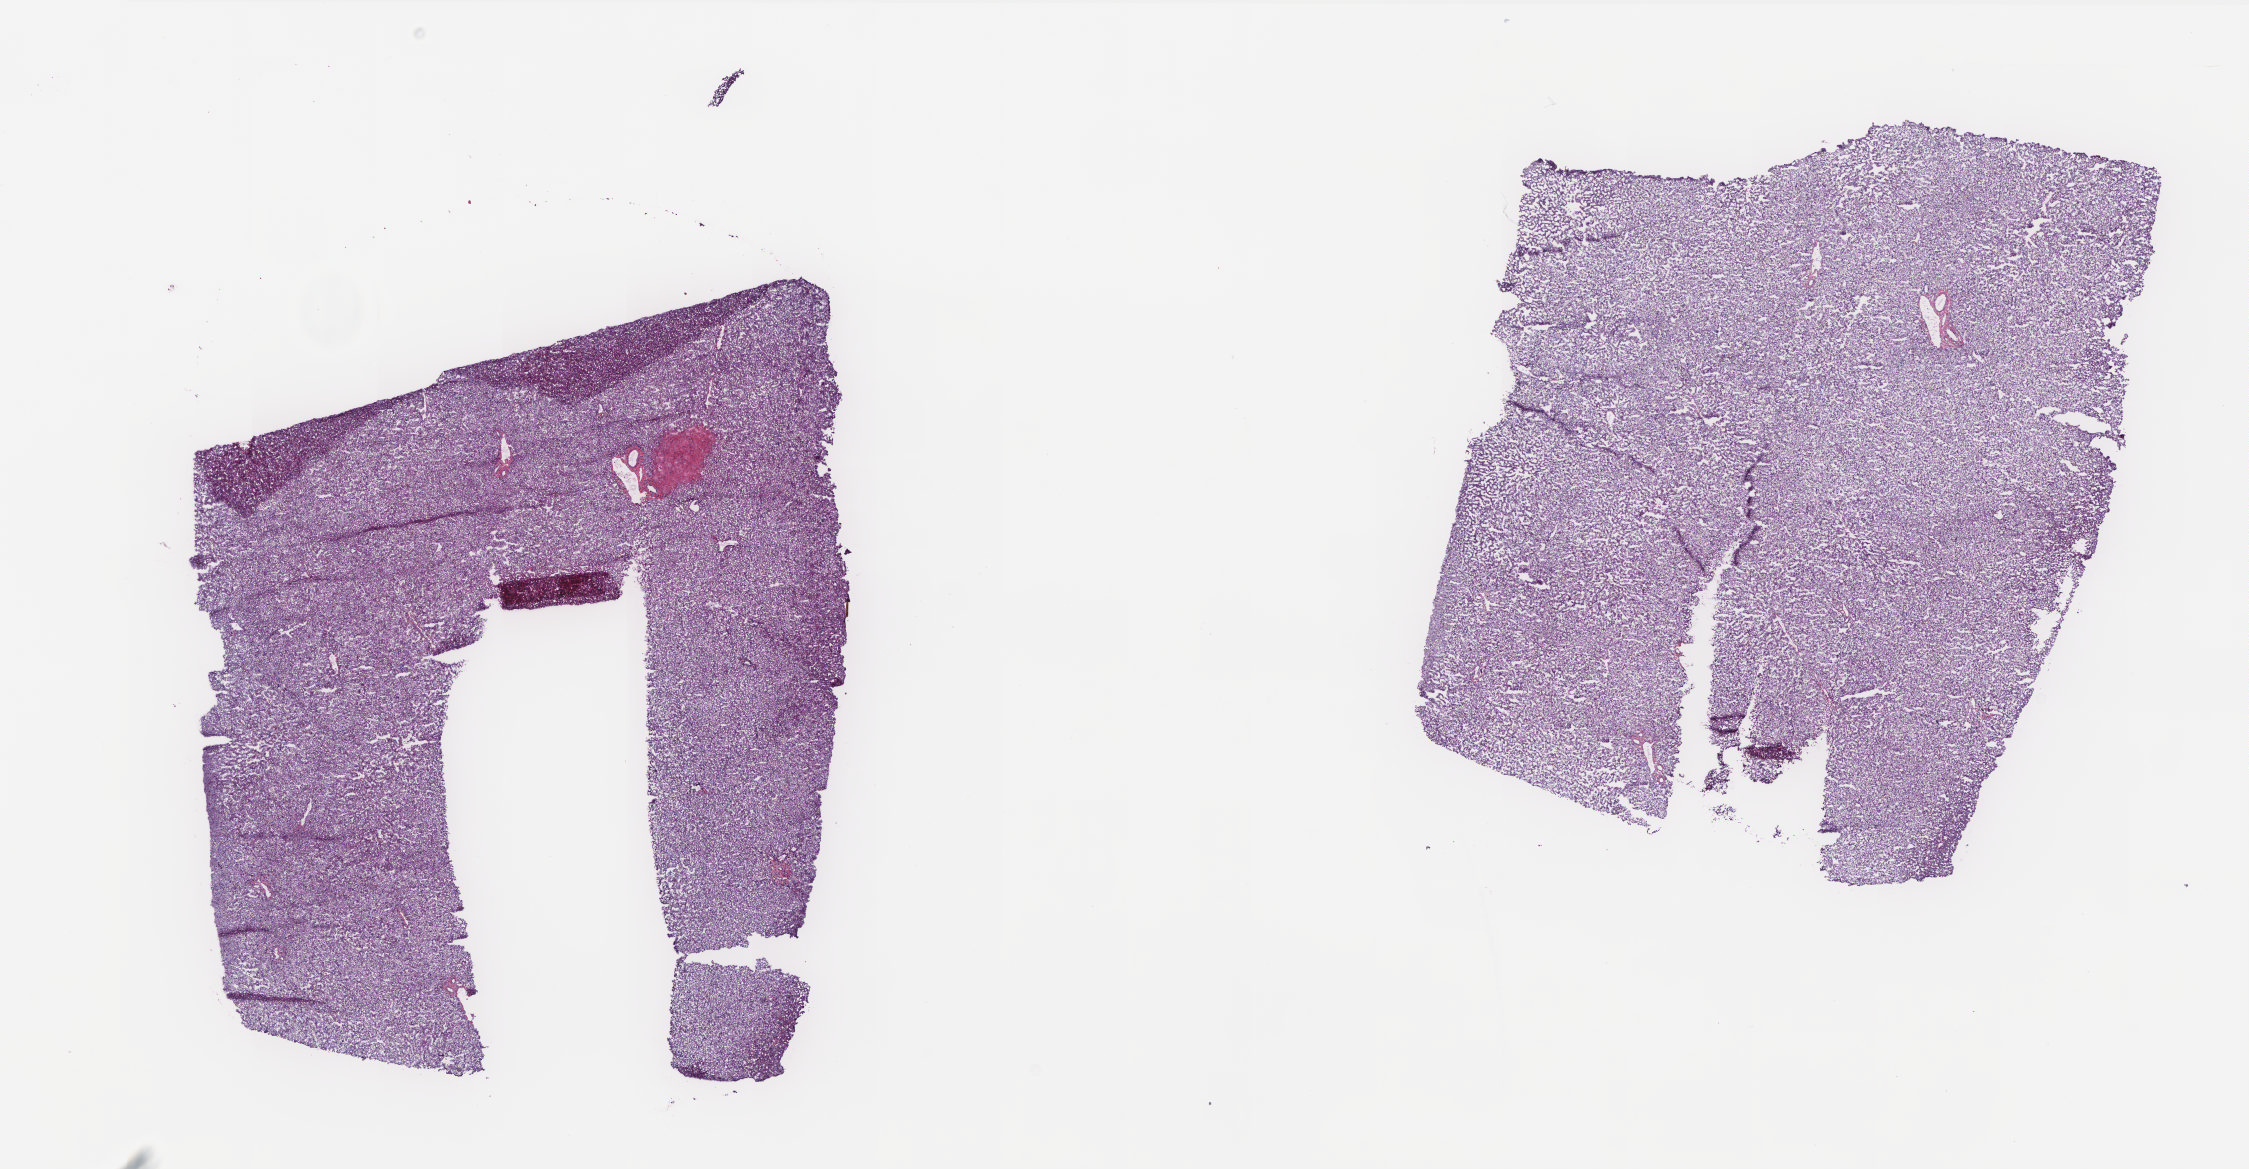
Digitized H&E tissue section (whole slide) — a low-resolution overview of the entire scanned area, about 18.0 x 9.3 mm (from a 20x scan). Frozen section. Sample: solid tissue normal (non-tumour tissue), liver. Female patient; age at initial diagnosis 29 years. Composition of this section per pathologist review: tumour cells 0%, tumour nuclei 0%, normal cells 85%, stromal cells 15%, necrosis 0%. Infiltration values recorded for this section: lymphocyte infiltration 2%, monocyte infiltration 1%, neutrophil infiltration 0%.
This section: solid tissue normal (non-tumour) sample from the same patient. Patient diagnosis: Hepatocellular carcinoma, NOS.